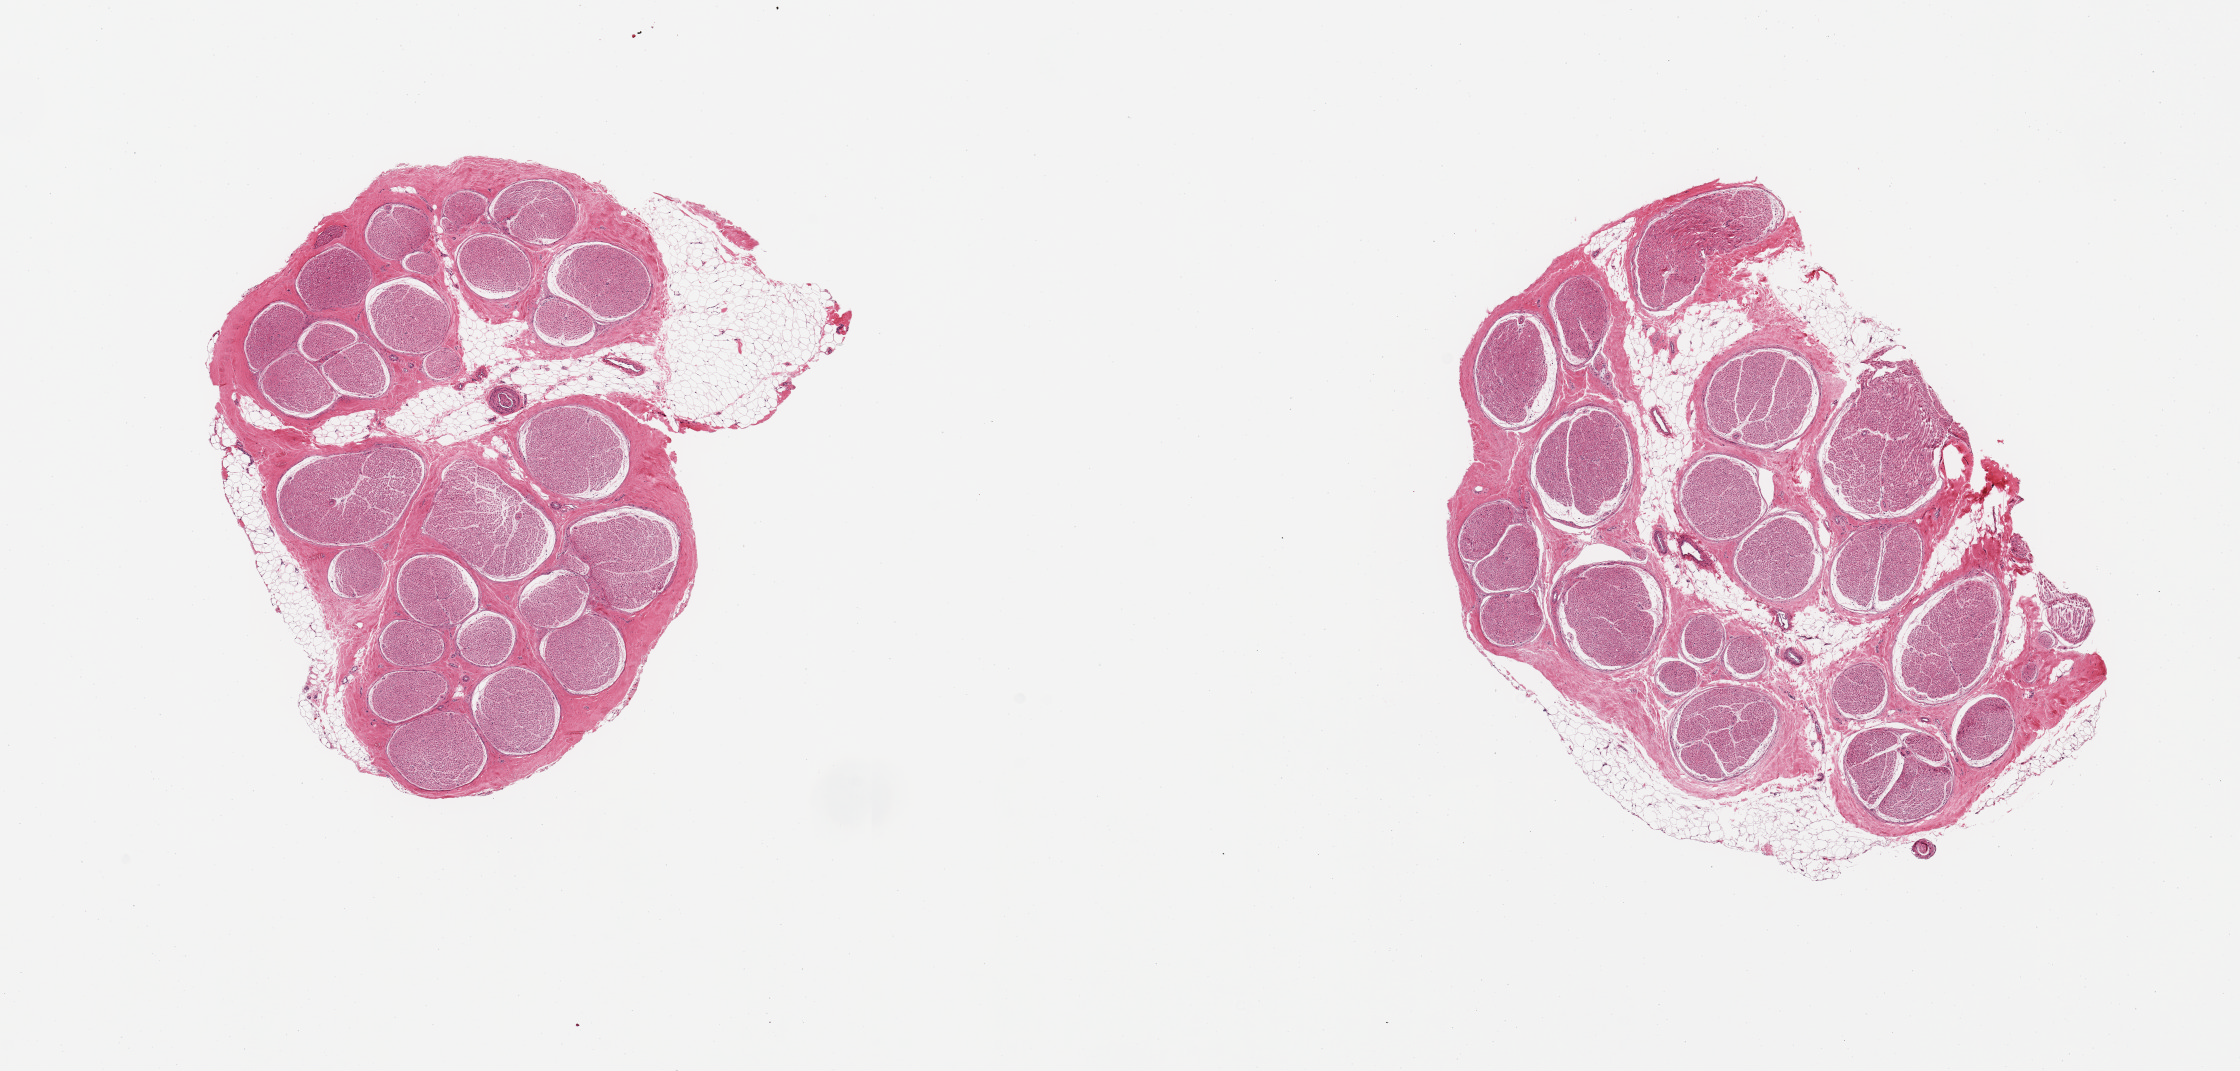
Hematoxylin and eosin (H&E) whole-slide image, shown as a low-resolution overview of the whole scanned area (about 17.7 x 8.5 mm). PAXgene-fixed paraffin-embedded (PFPE) section. Target tissue: tibial nerve. Tissue donor sample. Donor sex: male.
Review note (as recorded): 2 pieces; includes ~20% attached and internal fat.